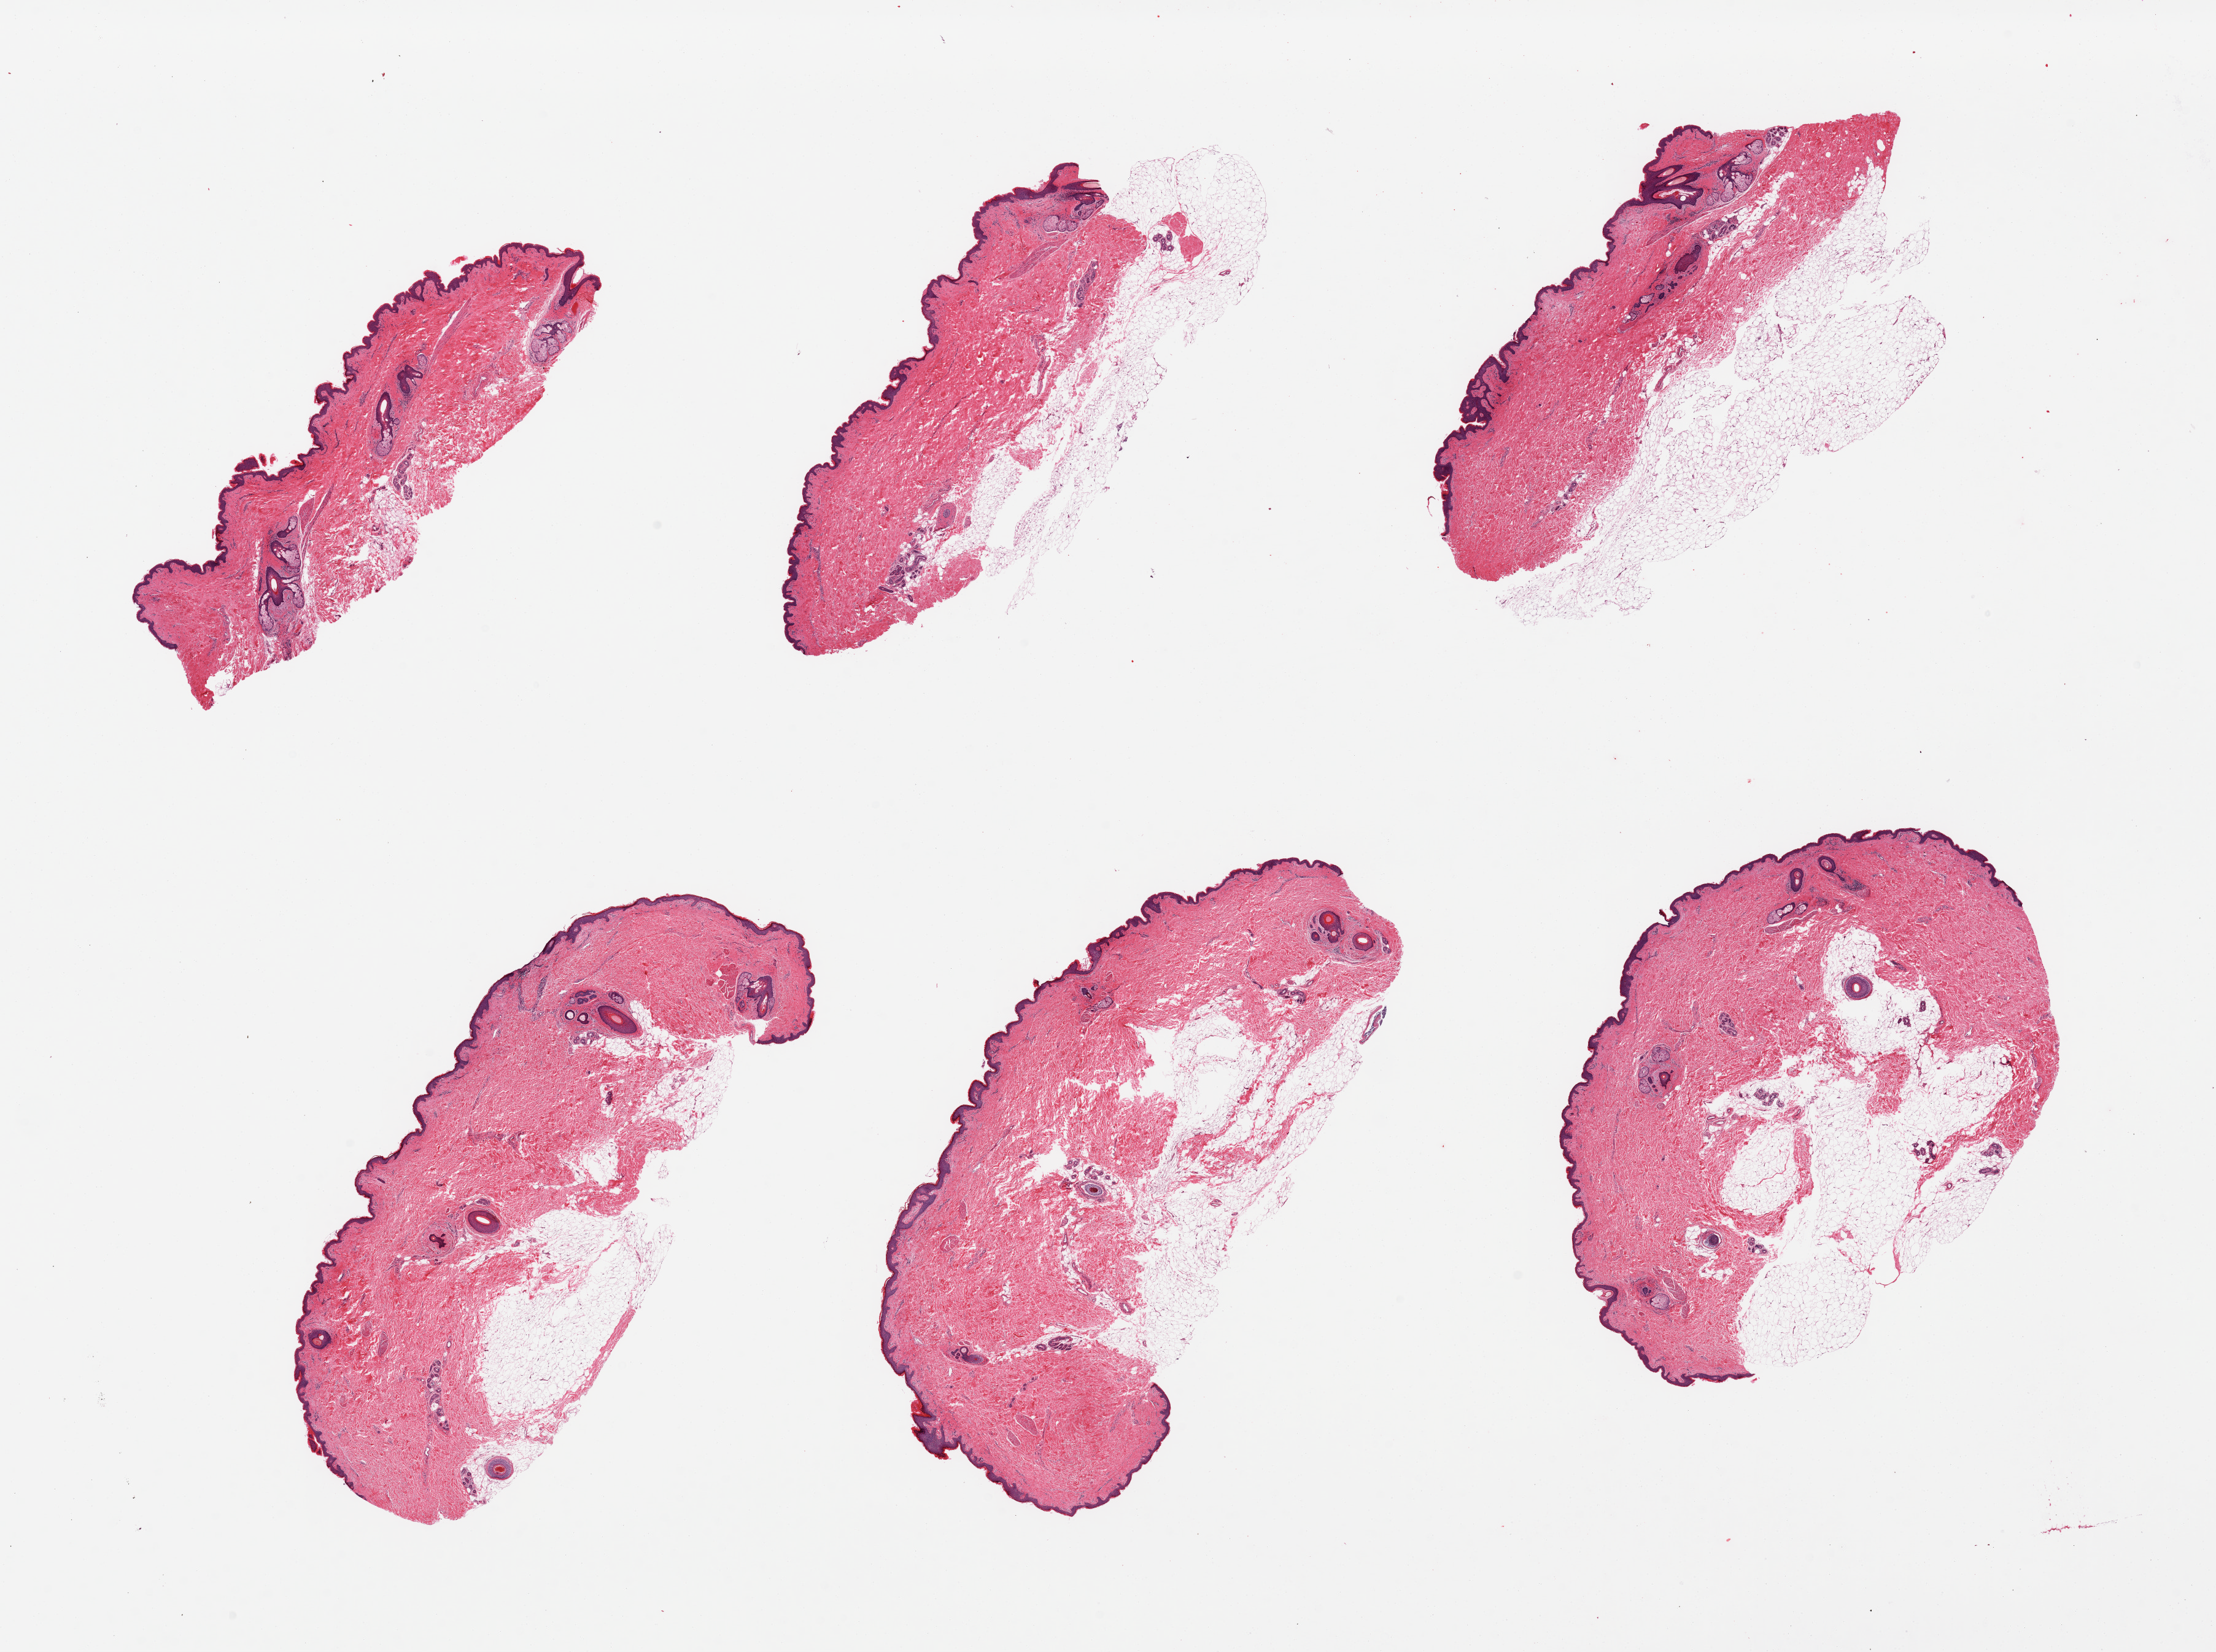
Digitized hematoxylin and eosin (H&E)-stained section — a low-resolution overview of the entire scanned area, about 28.5 x 21.3 mm, PAXgene-fixed paraffin-embedded (PFPE) section, section of skin of suprapubic region (target tissue), donor tissue sample. Donor: male.
Reviewer comment on this tissue sample: 6 pieces, up to 40% attached subcutaneous fat.